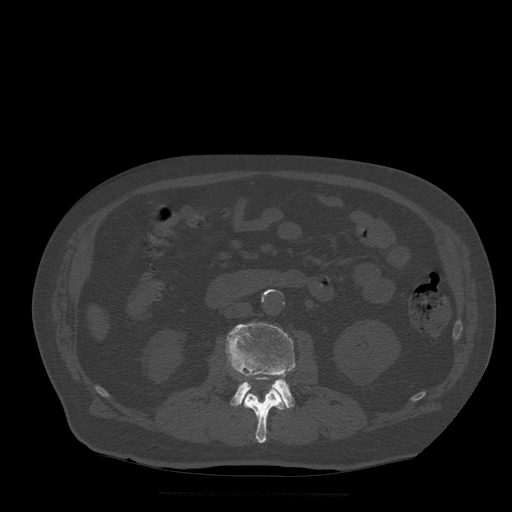
CT including the spine, one axial slice. Position 155 of 522 along the scan axis. Bone window (W 1800 / L 400 HU). 512 × 512 image matrix, field of view 420 × 420 mm. Patient age 72 years. Case-level facts recorded for this patient, not image findings: primary cancer: prostate.
Annotated regions visible in this slice (semi-automatic segmentation, software-assisted and operator-edited):
- L2 vertebra: bounding box <243,377,286,443> (left, top, right, bottom; pixels)
- L3 vertebra: <226,323,296,409>